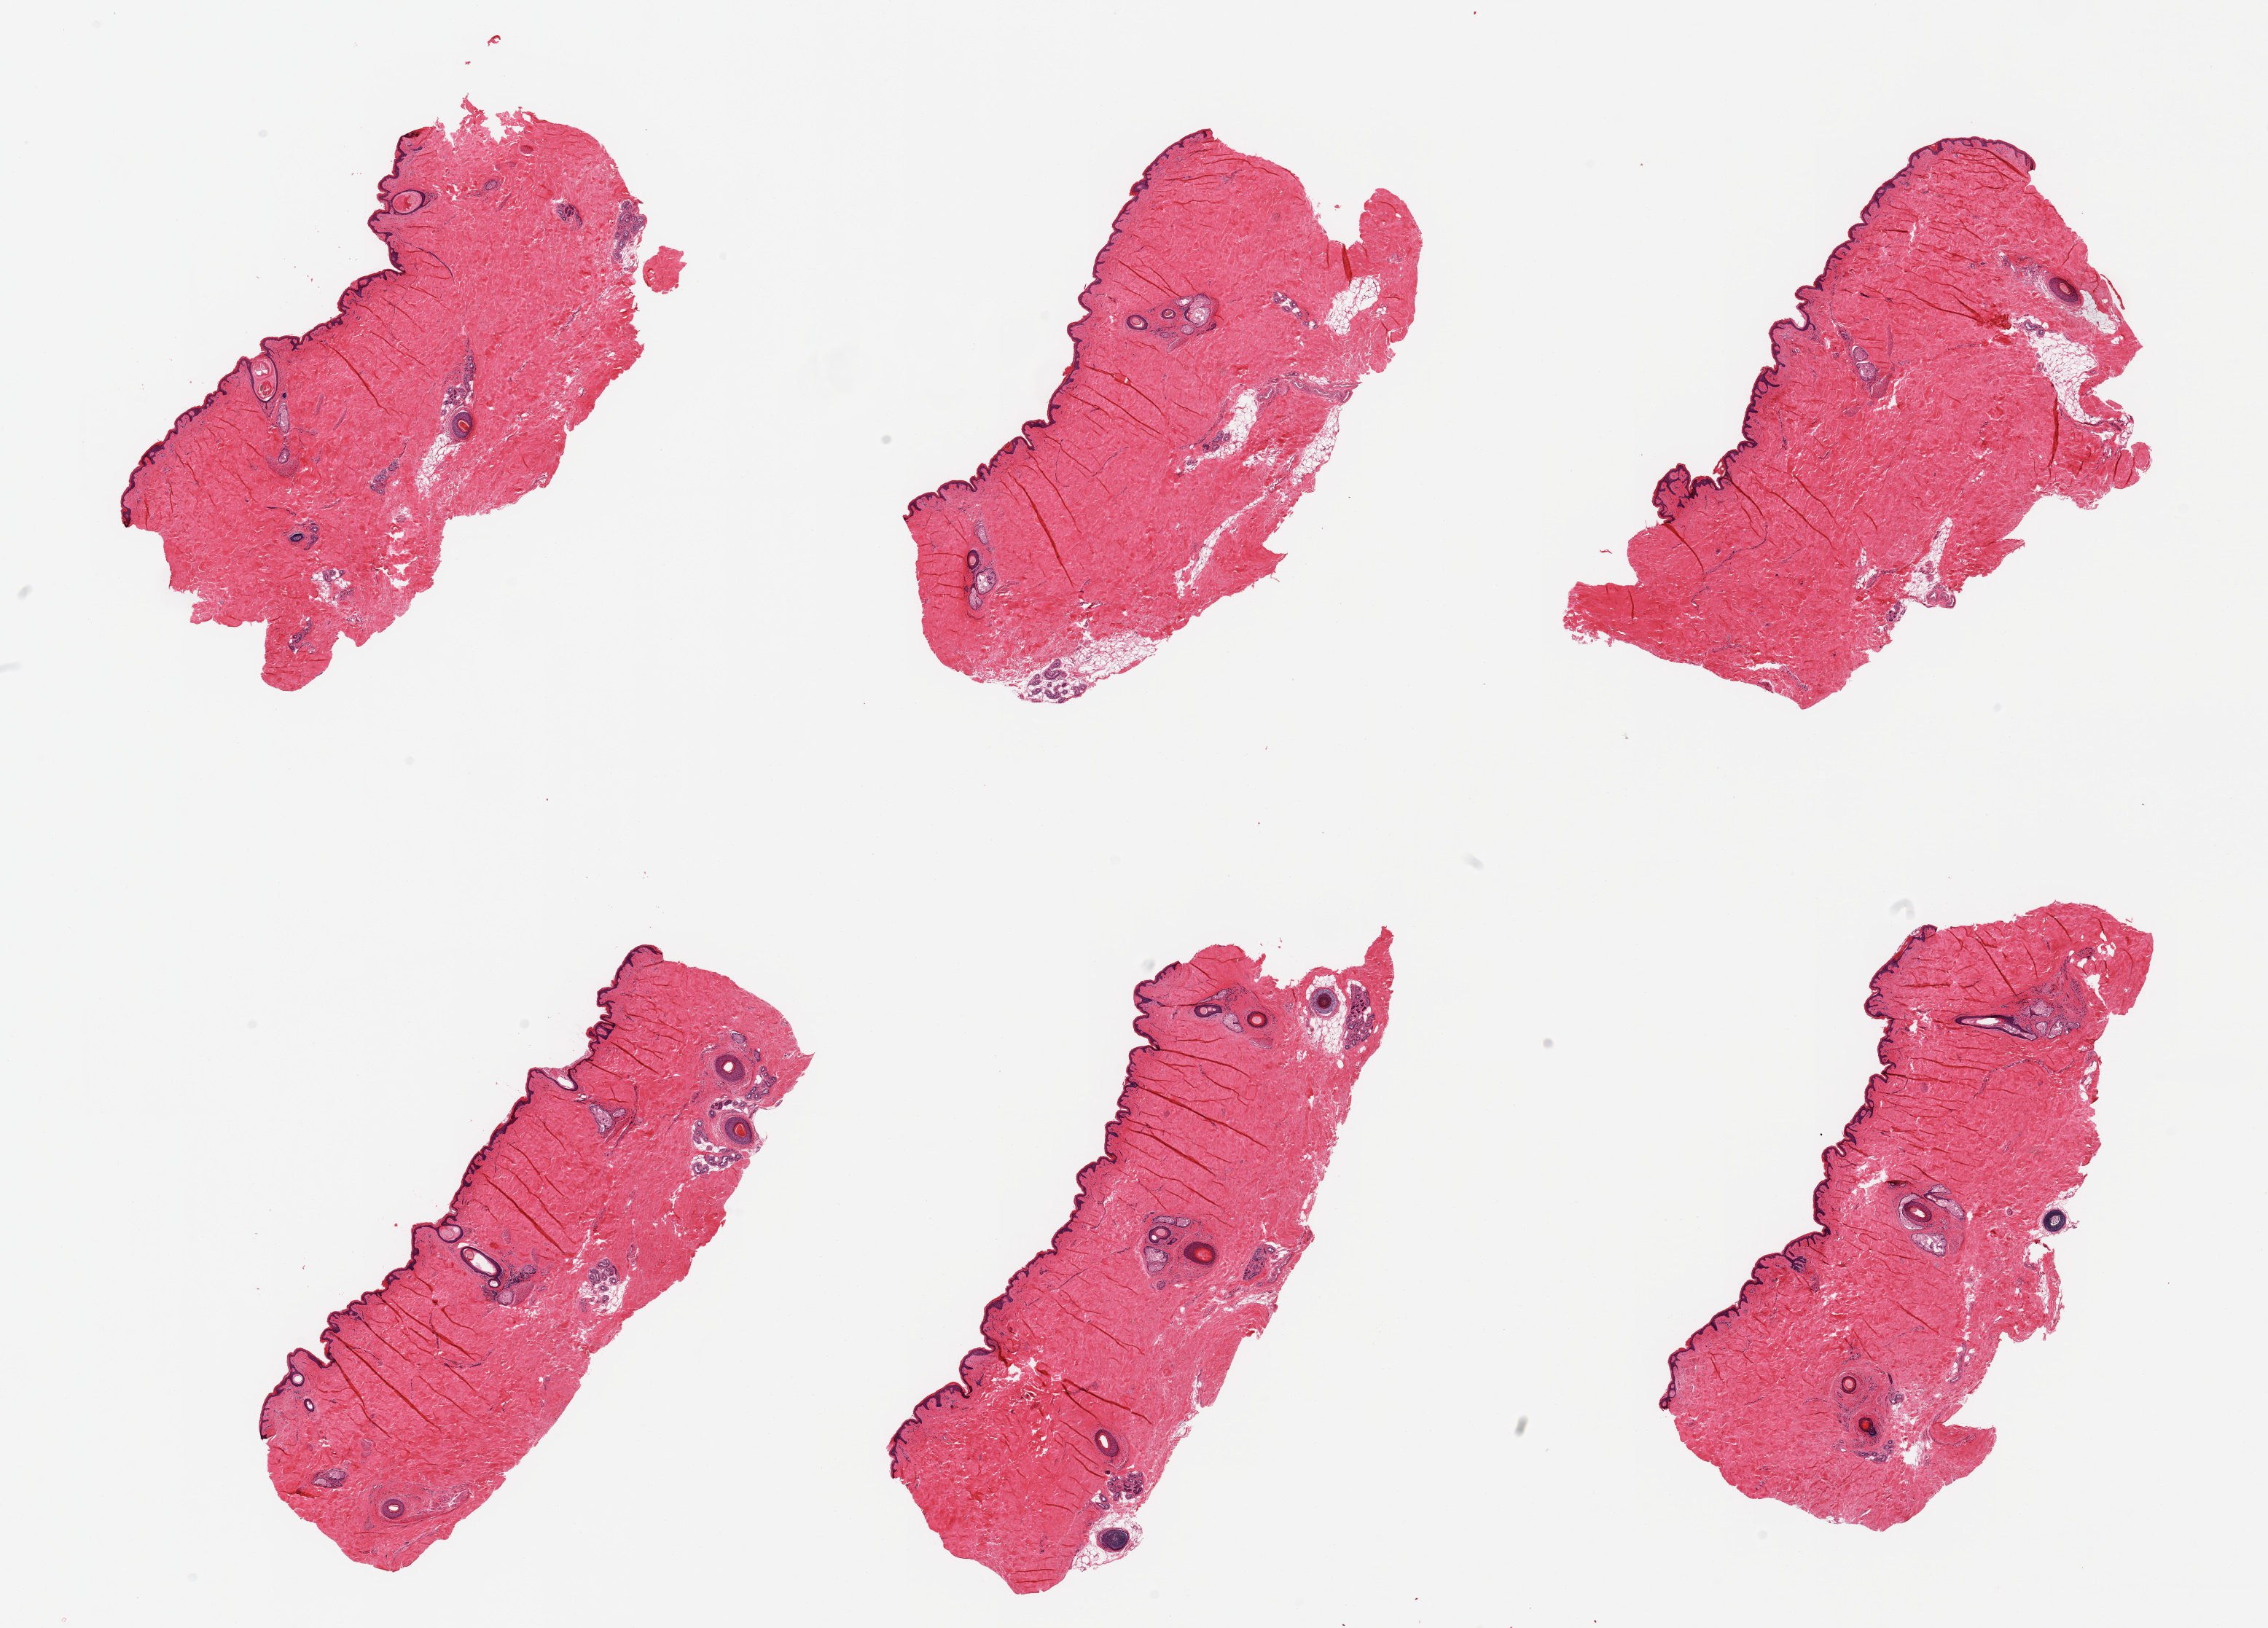
Whole-slide image, hematoxylin and eosin (H&E) stain — shown as a low-resolution overview of the whole scanned area (about 24.6 x 17.7 mm); PAXgene-fixed, paraffin-embedded tissue; section of skin of suprapubic region (target tissue); donor tissue sample. Male donor.
• pathologist's review note for this sample: 6 pieces, minimal dermal fat; squamous epithelium is ~35 microns